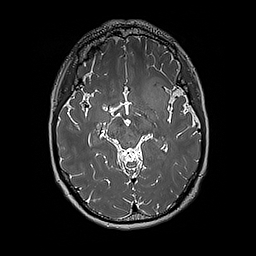
Brain MRI from a brain-tumour surgery series, one axial slice. Slice 110 of 192 in the series (ordered by position). 1 mm slice thickness. 256 × 256 image matrix, field of view 250 × 250 mm. Case-level facts recorded for this patient, not image findings: histopathology: Glioblastoma; WHO grade: 4; IDH mutation: no.
Structures marked on this image (outlined manually by an expert reader):
- tumour: box from (x=142, y=77) to (x=170, y=111) px